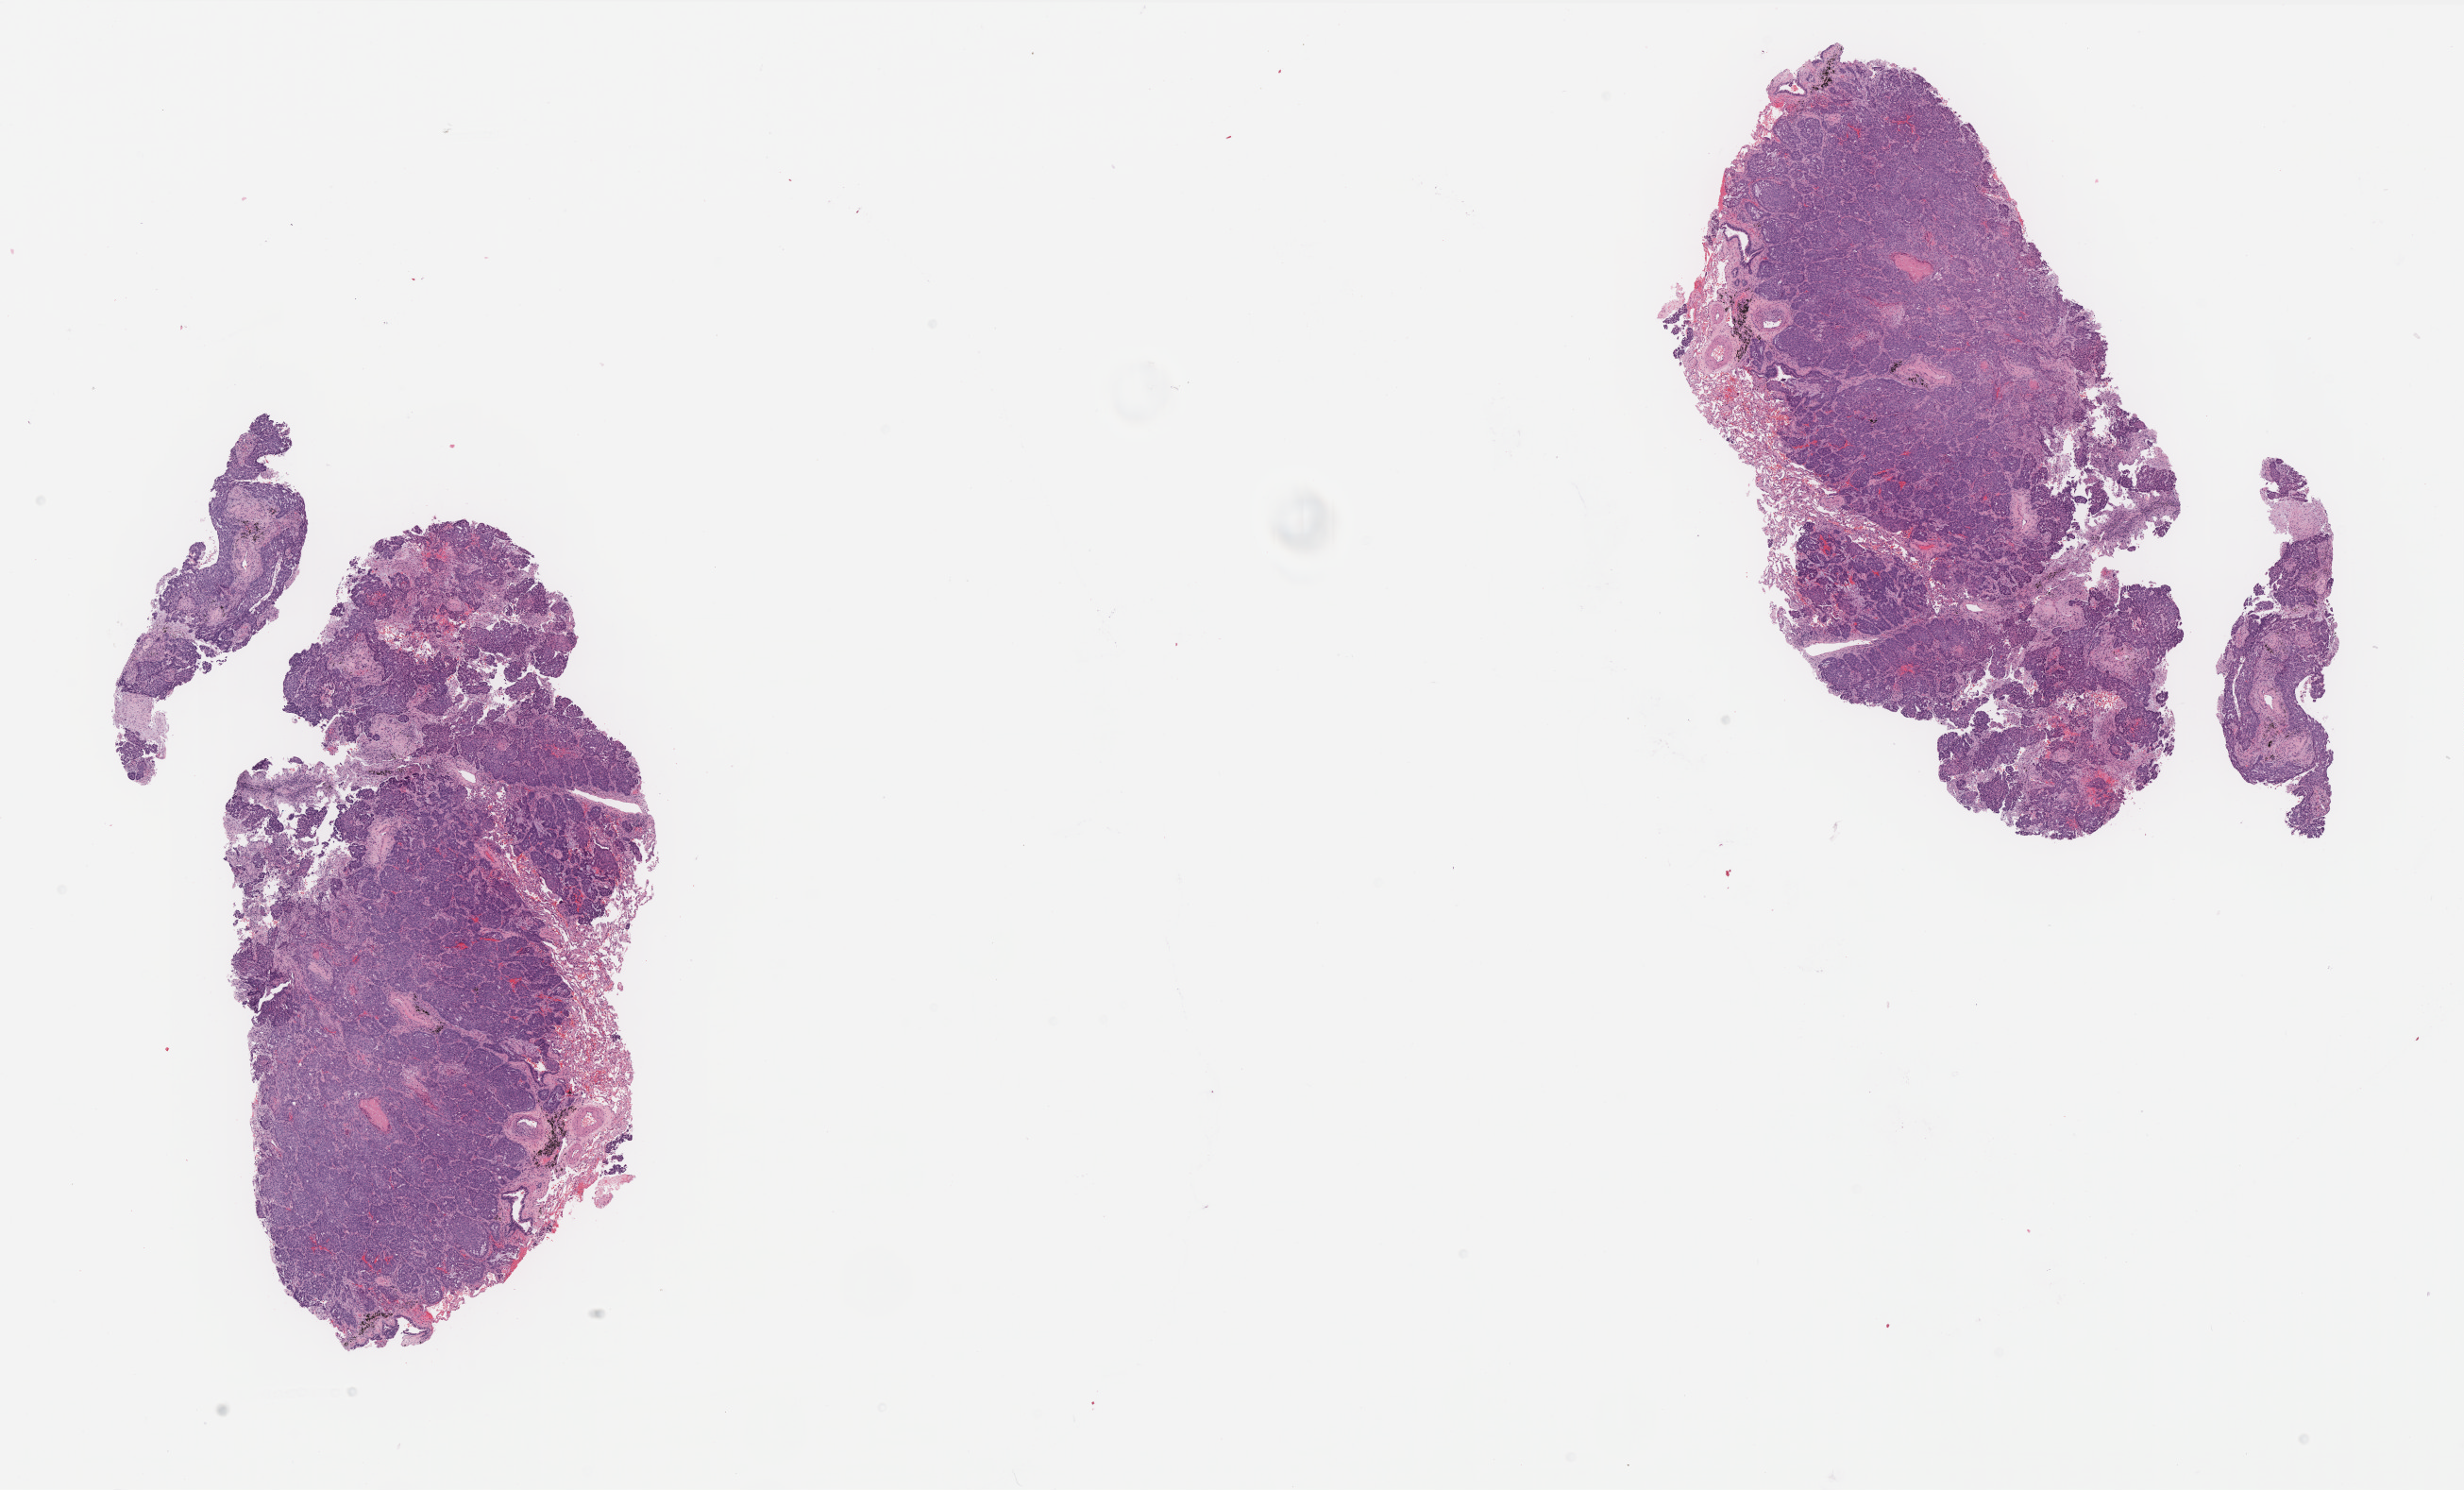
Digitized H&E-stained tissue section (whole slide), shown as a low-resolution overview of the whole scanned area (about 20.9 x 12.7 mm). Formalin-fixed paraffin-embedded (FFPE) diagnostic section. Primary tumour sample from the lung. Male patient; age at initial diagnosis 69 years.
Pathologic diagnosis: Squamous cell carcinoma, NOS. AJCC pathologic stage: IB (7th edition).